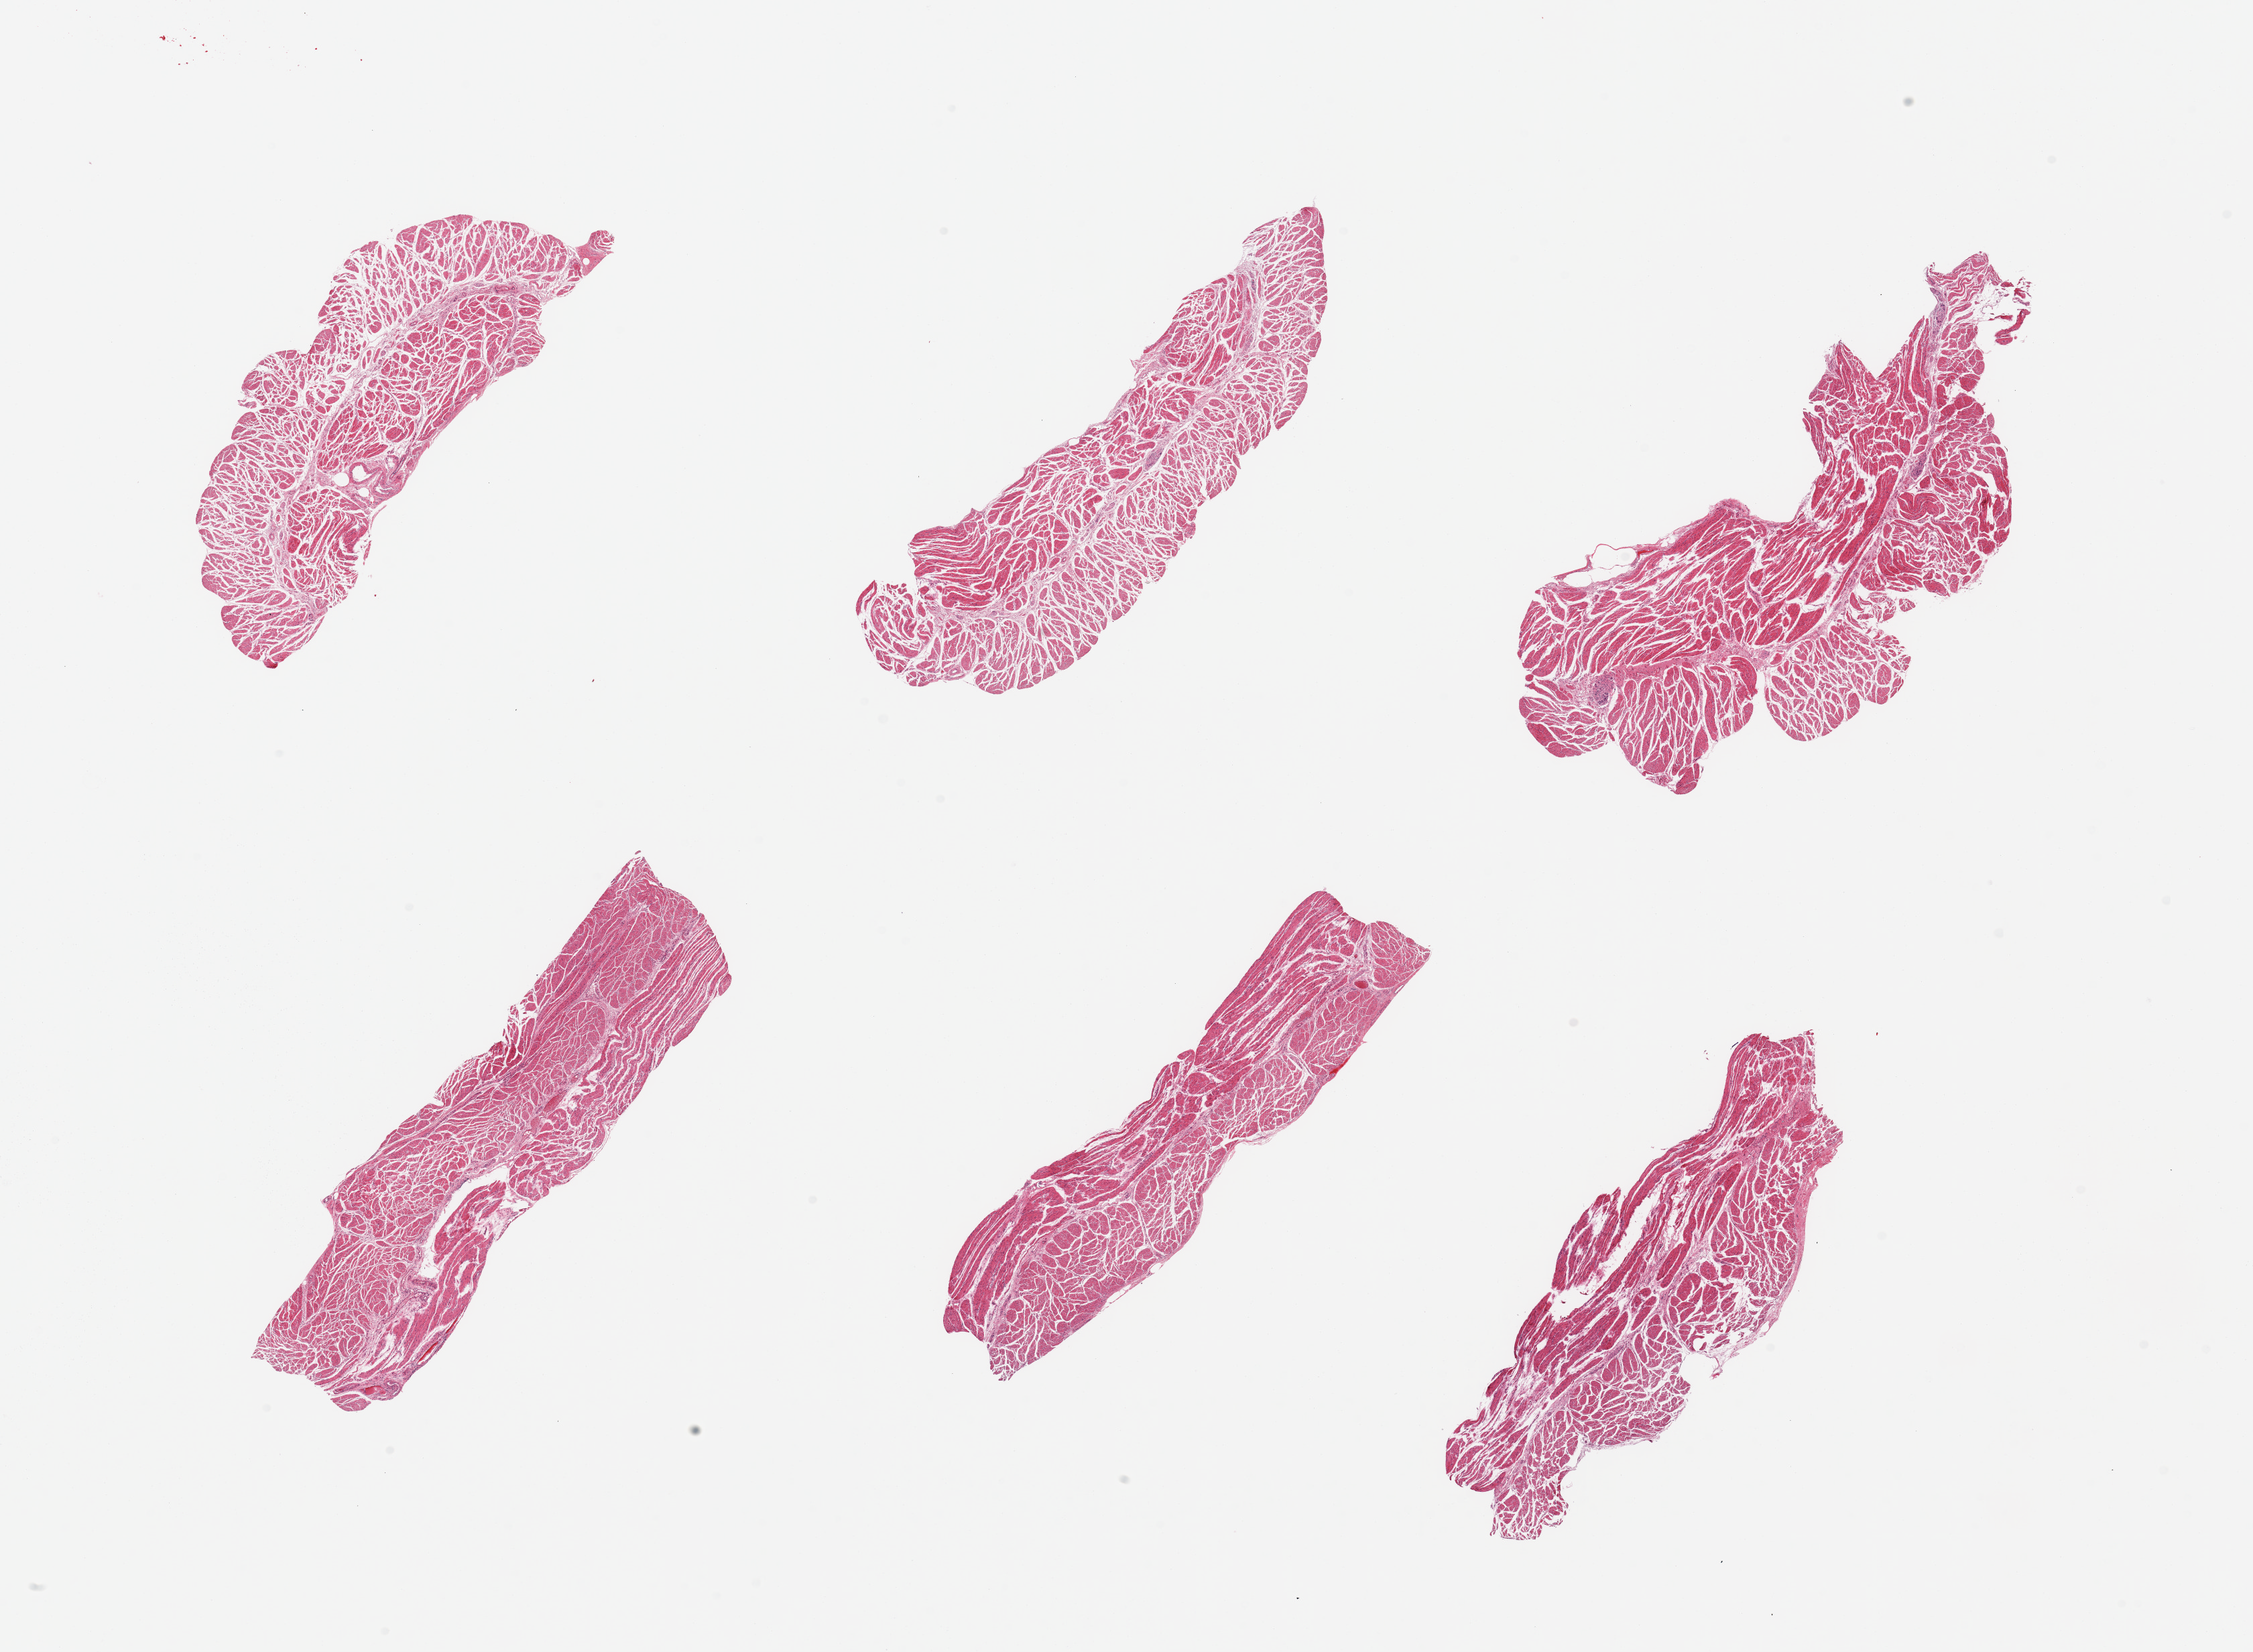
Whole-slide image, hematoxylin and eosin (H&E) stain — low-resolution overview of the scanned area, about 26.6 x 19.5 mm, PAXgene-fixed paraffin-embedded (PFPE) section, section of esophageal muscle (target tissue), donor tissue sample. Male donor.
Review note (as recorded): 6 pieces; well dissected muscularis.